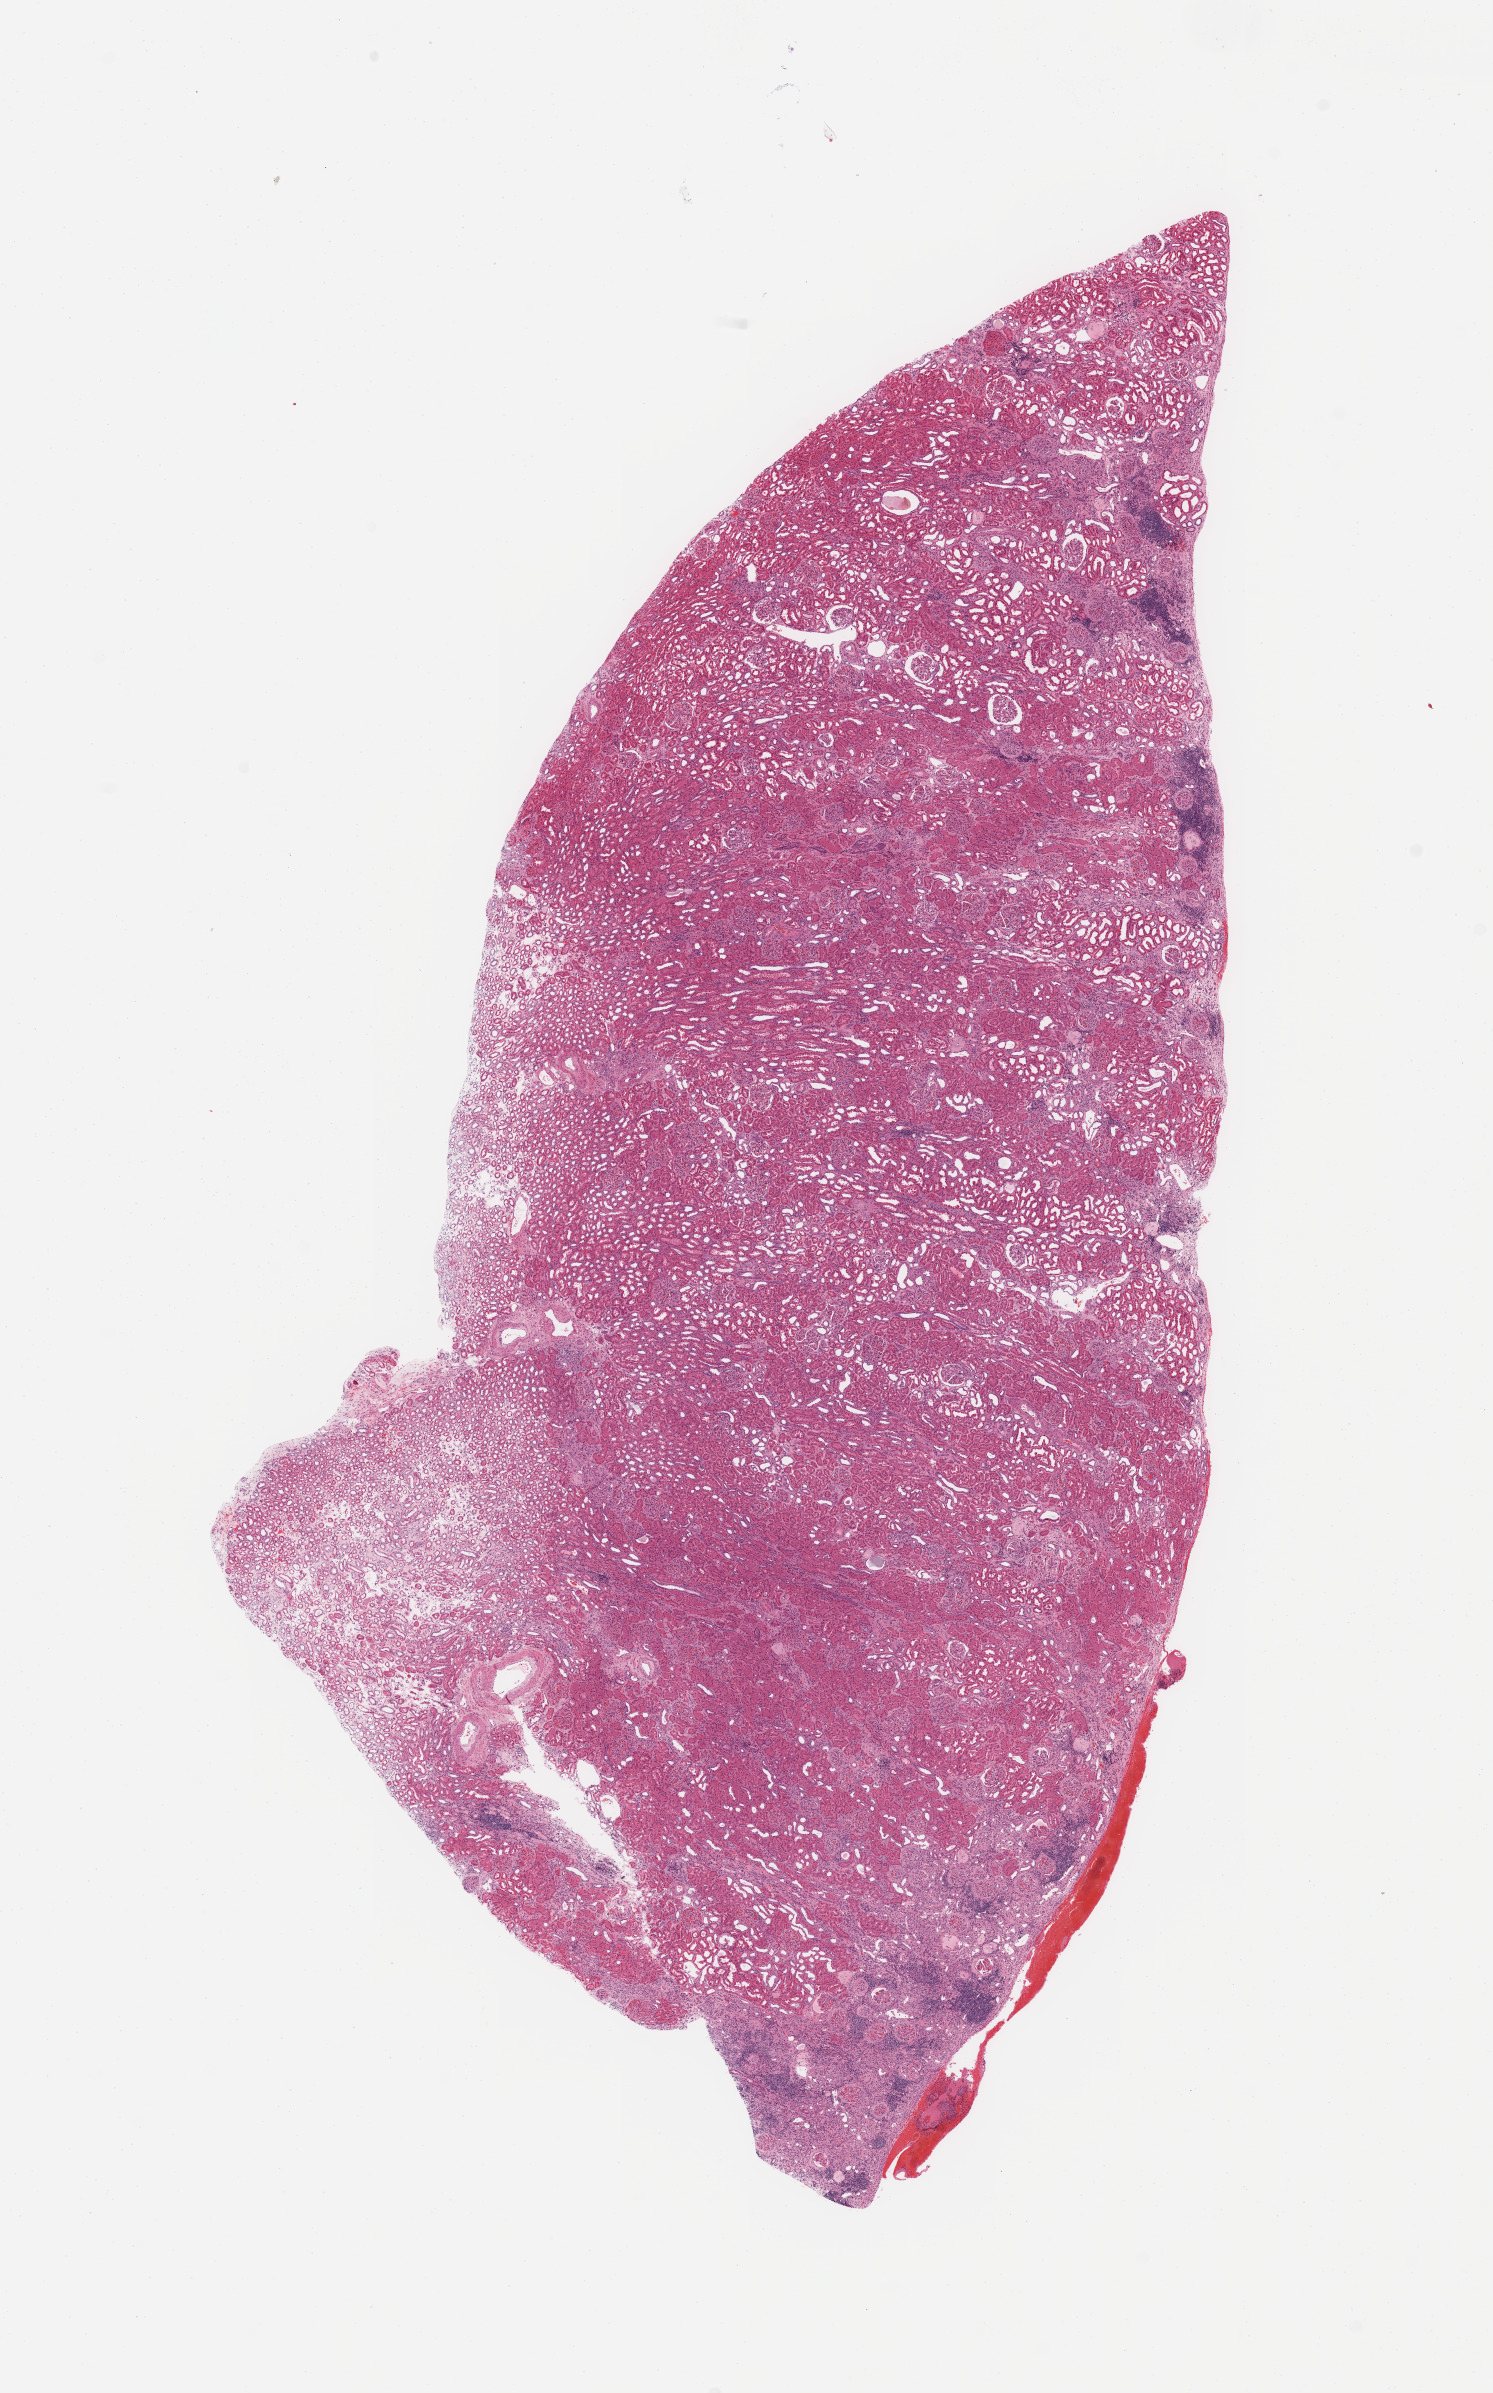
Whole-slide histology image, Hematoxylin and eosin (H&E) stained, low-resolution overview of the scanned area, about 11.8 x 18.9 mm (acquisition: 20x scan); normal (non-tumour) tissue sample, sampled site: kidney. Patient: male, age 50 years.
This section: normal (non-tumour) tissue from the same patient. Patient diagnosis: Renal cell carcinoma, NOS.